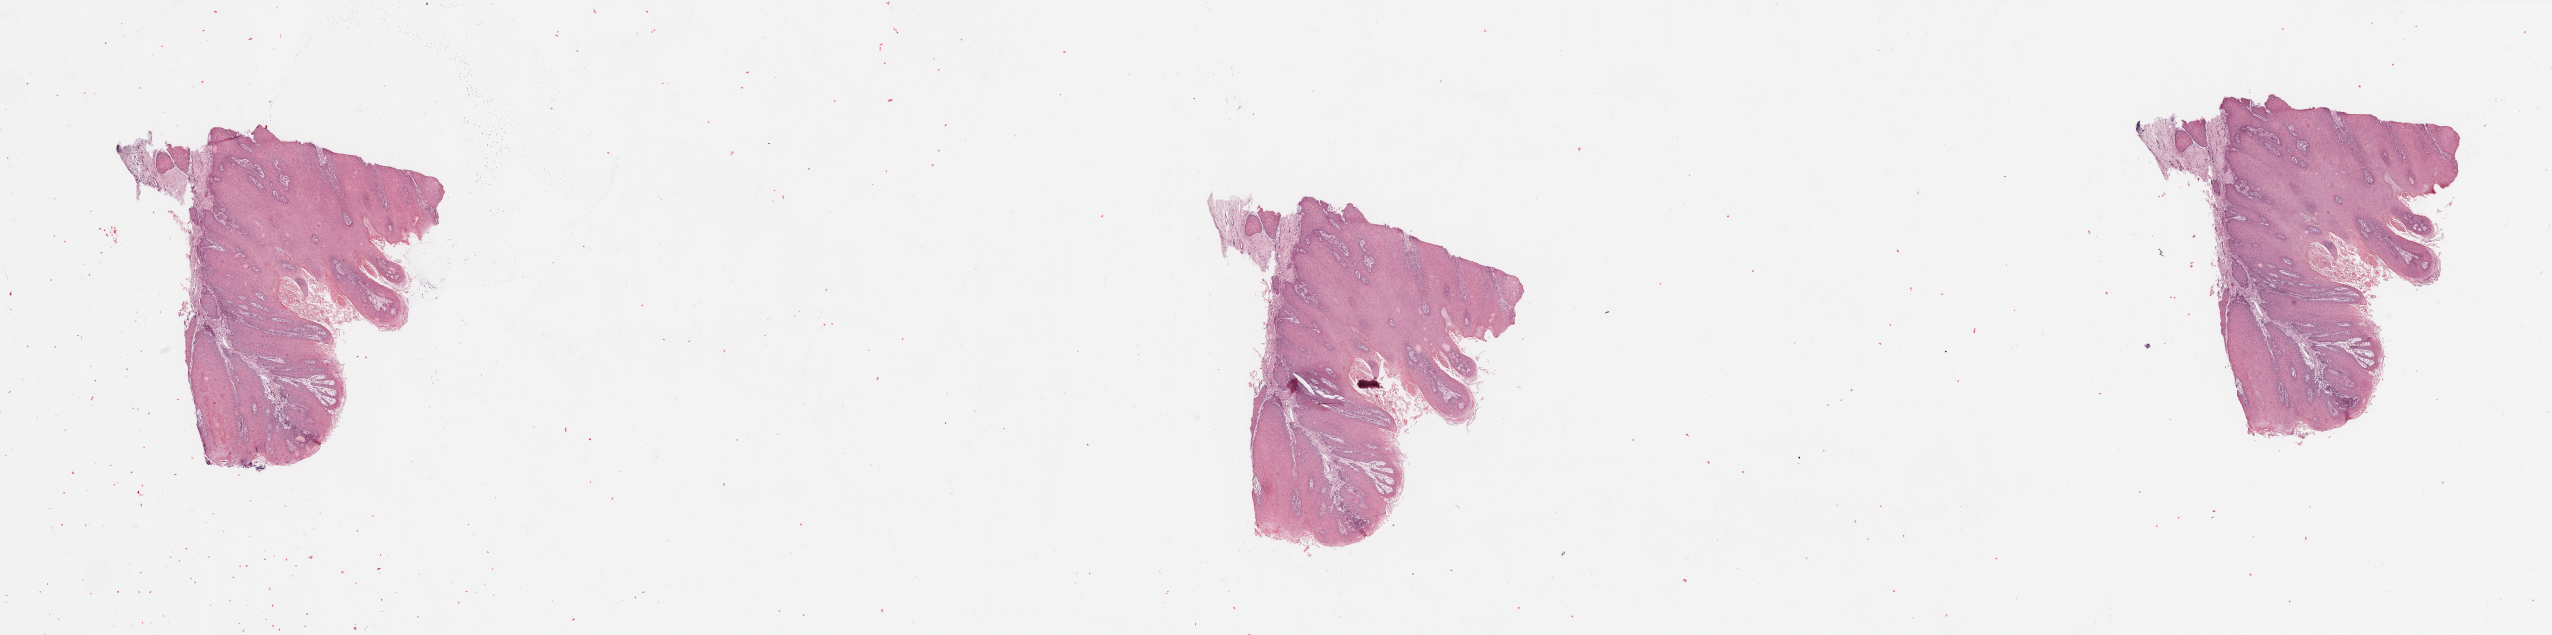
Hematoxylin and eosin (H&E) stained whole-slide image, a low-resolution overview of the entire scanned area, about 40.4 x 10.0 mm (from a 20x scan); tumour tissue sample, sampled site: larynx. 65-year-old male patient. Histologic grade: G1 (well differentiated). Composition of this section per pathologist review: tumour nuclei 85%, necrosis 5%.
* primary tumour site (as recorded): larynx
* histologic diagnosis: Squamous cell carcinoma, NOS (larynx, NOS)
* AJCC pathologic stage: II